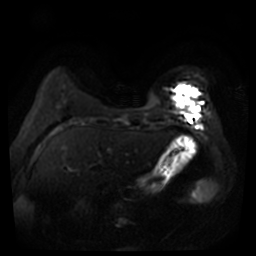
Breast MRI, one axial slice. Position 10 of 44 along the scan axis. Diffusion-weighted series; image 2 of 4 stored at this slice position (different b-values; order by instance number). 3 T. 5 mm slice thickness. 256 × 256 image matrix. Female patient.
Outlined on this slice (expert manual segmentation):
- tumour on diffusion-weighted imaging: bounding box (x1, y1, x2, y2) in pixels: (175, 88, 197, 112)